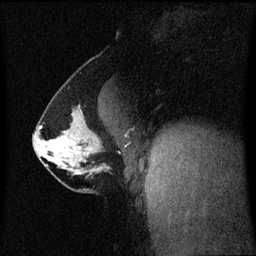
Breast MRI (dynamic contrast-enhanced), one sagittal slice. Slice 31 of 60 in the series (ordered by position). Dynamic contrast-enhanced series, image 2 of 3 at this slice position (ordered by acquisition). 1.5 T. TE 4.2 ms, TR 8.4 ms. 2 mm slice thickness. 256 × 256 image matrix. Patient: female, 40 years. From the clinical record (not read from this slice): setting: breast cancer imaged before/during neoadjuvant chemotherapy; receptor status: triple-negative.
Annotated regions visible in this slice (semi-automatically segmented with operator editing):
- analysis volume of interest (the breast-tissue region the enhancement analysis was run in; not a lesion): box from (x=33, y=112) to (x=118, y=188) px
- tumour enhancement mask (voxels above the 70 % enhancement threshold inside the analysis volume of interest): (x=40, y=127)–(x=80, y=151)